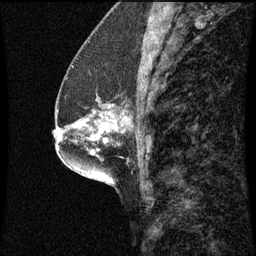
Breast MRI (dynamic contrast-enhanced), one sagittal slice; dynamic contrast-enhanced series, image 2 of 3 at this slice position (ordered by acquisition); 1.5 T; TE 4.2 ms, TR 8.9 ms; 2 mm slice thickness; 256 × 256 image matrix. Patient: female, 57 years. Case-level facts recorded for this patient, not image findings: setting: breast cancer imaged before/during neoadjuvant chemotherapy; receptor status: HR-positive, HER2-negative.
Annotated regions visible in this slice (semi-automatically segmented with operator editing):
- analysis volume of interest (the breast-tissue region the enhancement analysis was run in; not a lesion): bounding box <82,90,124,125> (left, top, right, bottom; pixels)
- tumour enhancement mask (voxels above the 70 % enhancement threshold inside the analysis volume of interest): <113,120,118,123>